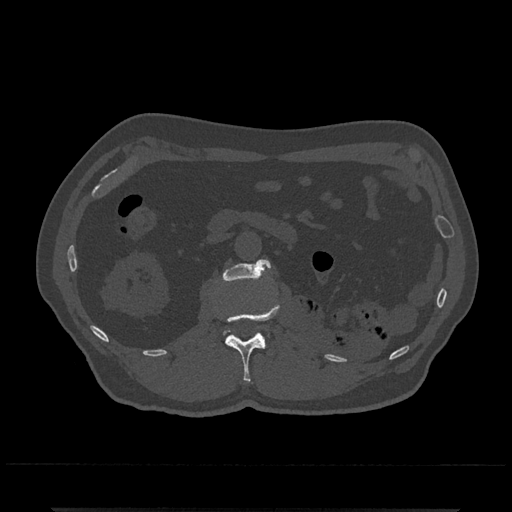
CT including the spine, one axial slice; slice 337 of 797 in the series (ordered by position); reconstruction kernel Br40s/3; 120 kVp; bone window (W 1800 / L 400 HU); 512 × 512 image matrix, field of view 393 × 393 mm. Male patient, age 67 years. From the clinical record (not read from this slice): primary cancer: prostate.
Structures marked on this image (semi-automatically segmented with operator editing):
- L1 vertebra: bounding box (x1, y1, x2, y2) in pixels: (225, 305, 279, 383)
- L2 vertebra: (221, 259, 271, 341)